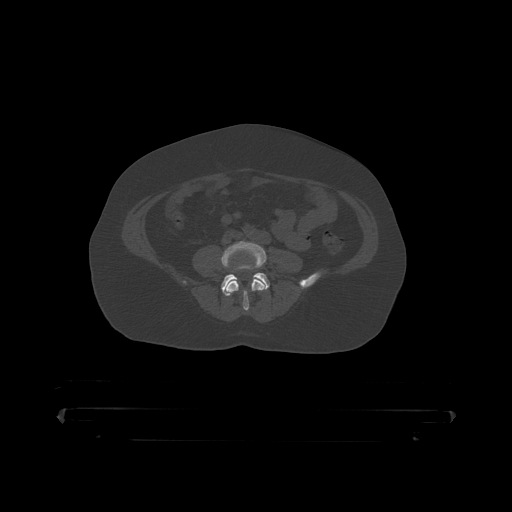
CT including the spine, one axial slice; position 53 of 390 along the scan axis; reconstruction kernel STANDARD; 120 kVp; bone window (W 1800 / L 400 HU); 1.25 mm slice thickness; 512 × 512 image matrix, field of view 650 × 650 mm. Patient: male, 60 years. From the clinical record (not read from this slice): primary cancer: prostate.
Outlined on this slice (semi-automatically segmented with operator editing):
- L4 vertebra: bounding box (x1, y1, x2, y2) in pixels: (222, 241, 266, 312)
- L5 vertebra: (221, 273, 270, 296)